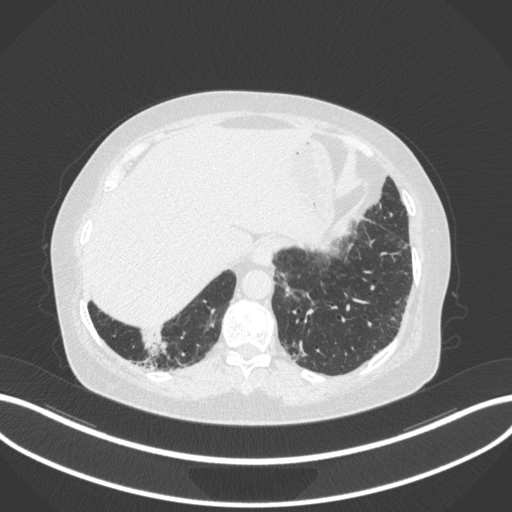
Chest CT, one axial slice; position 17 of 303 along the scan axis; reconstruction kernel B31f; lung window (W 1500 / L -600 HU); 1 mm slice thickness; 512 × 512 image matrix, field of view 400 × 400 mm. Female patient, age 65 years. From the clinical record (not read from this slice): clinical TNM (as recorded): T2b N1 M0; histopathological grade: G1.
Outlined on this slice (rectangle marked by the reading radiologist):
- lung tumour (recorded histology: adenocarcinoma): bounding box (x1, y1, x2, y2) in pixels: (137, 328, 171, 361)